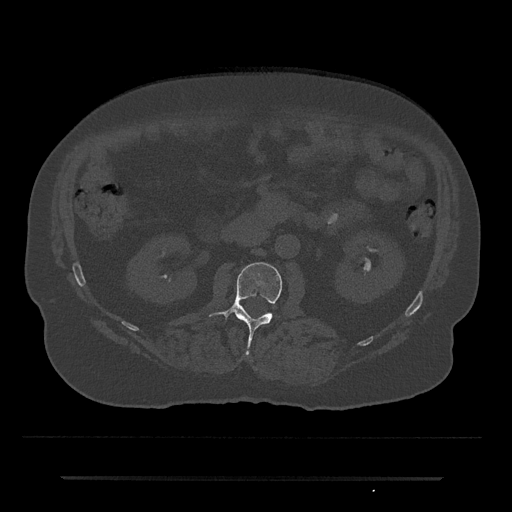
CT including the spine, one axial slice; slice 8 of 797 in the series (ordered by position); reconstruction kernel Br40s/3; bone window (W 1800 / L 400 HU); 0.5 mm slice thickness; 512 × 512 image matrix, field of view 437 × 437 mm. Male patient, age 69 years. From the clinical record (not read from this slice): primary cancer: prostate.
Outlined on this slice (semi-automatic segmentation, software-assisted and operator-edited):
- L2 vertebra: bounding box [x1, y1, x2, y2] px = [209, 262, 282, 354]